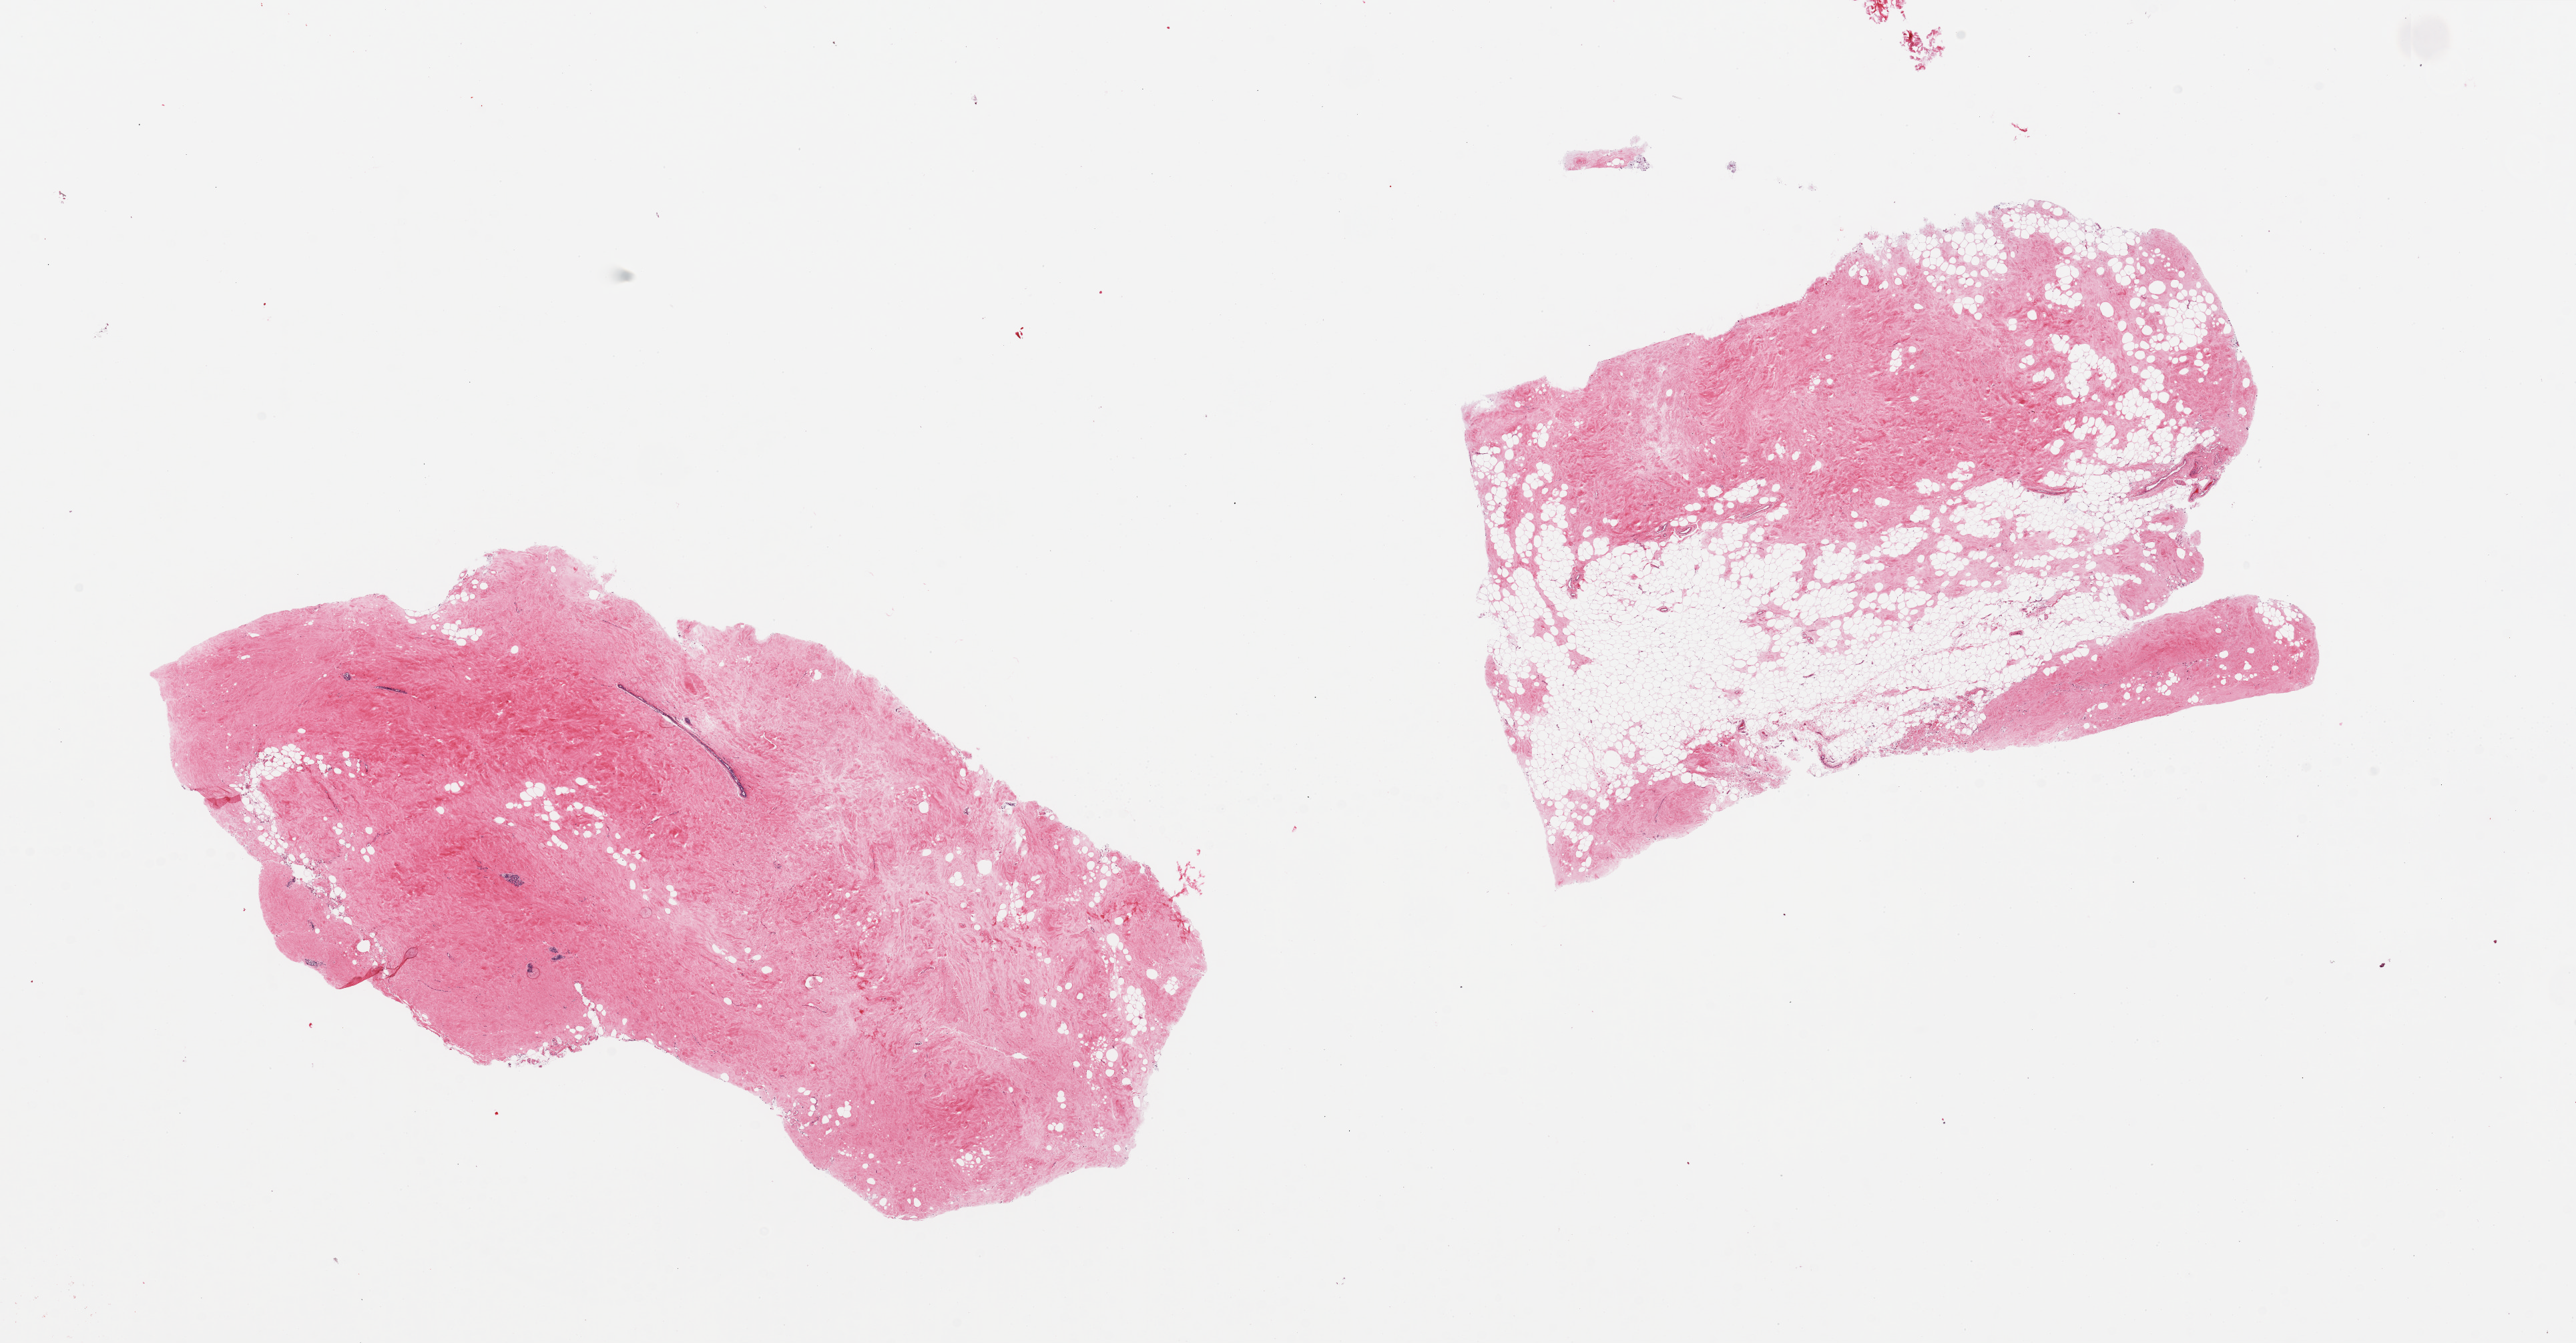
Digitized H&E-stained section, brightfield, shown as a low-resolution overview of the whole scanned area (about 30.5 x 15.9 mm). PAXgene-fixed paraffin-embedded (PFPE) section. Sampled site (target tissue): breast. Donor tissue sample. Donor sex: female.
• review note (as recorded): 2 pieces, a few minute atrophic lobular units, largely fibrous mastopathy/adipose tissue